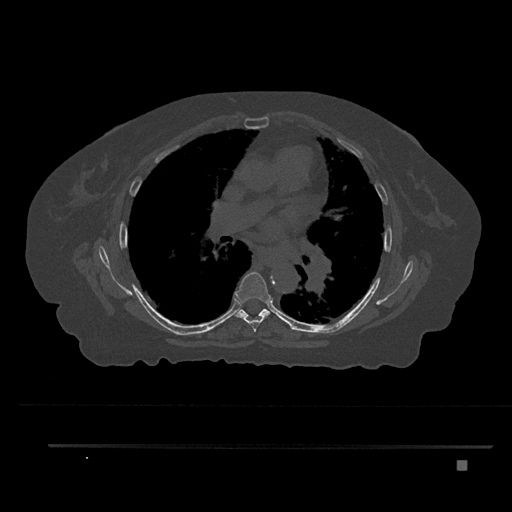
CT including the spine, one axial slice. Slice 513 of 797 in the series (ordered by position). Reconstruction kernel Br40s/3. 120 kVp. Bone window (W 1800 / L 400 HU). 0.5 mm slice thickness. 512 × 512 image matrix. Female patient, age 76 years. Case-level facts recorded for this patient, not image findings: primary cancer: lung; vertebrae with lytic lesions (as recorded): T11, L3.
Outlined on this slice (semi-automatic segmentation, software-assisted and operator-edited):
- T6 vertebra: bounding box [x1, y1, x2, y2] px = [234, 271, 271, 332]
- T7 vertebra: [238, 309, 270, 317]